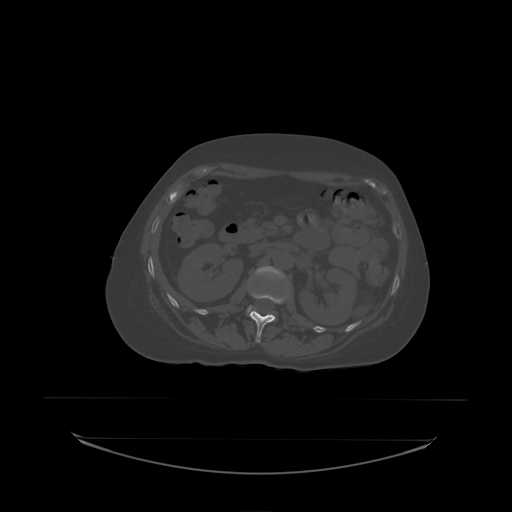
CT including the spine, one axial slice; bone window (W 1800 / L 400 HU); 512 × 512 image matrix, field of view 500 × 500 mm. Patient: female, 53 years. From the clinical record (not read from this slice): primary cancer: lung; vertebrae with lytic lesions (as recorded): T7, L1.
Structures marked on this image (semi-automatically segmented with operator editing):
- L1 vertebra: box from (x=250, y=294) to (x=283, y=338) px
- L2 vertebra: (x=247, y=266)–(x=287, y=319)